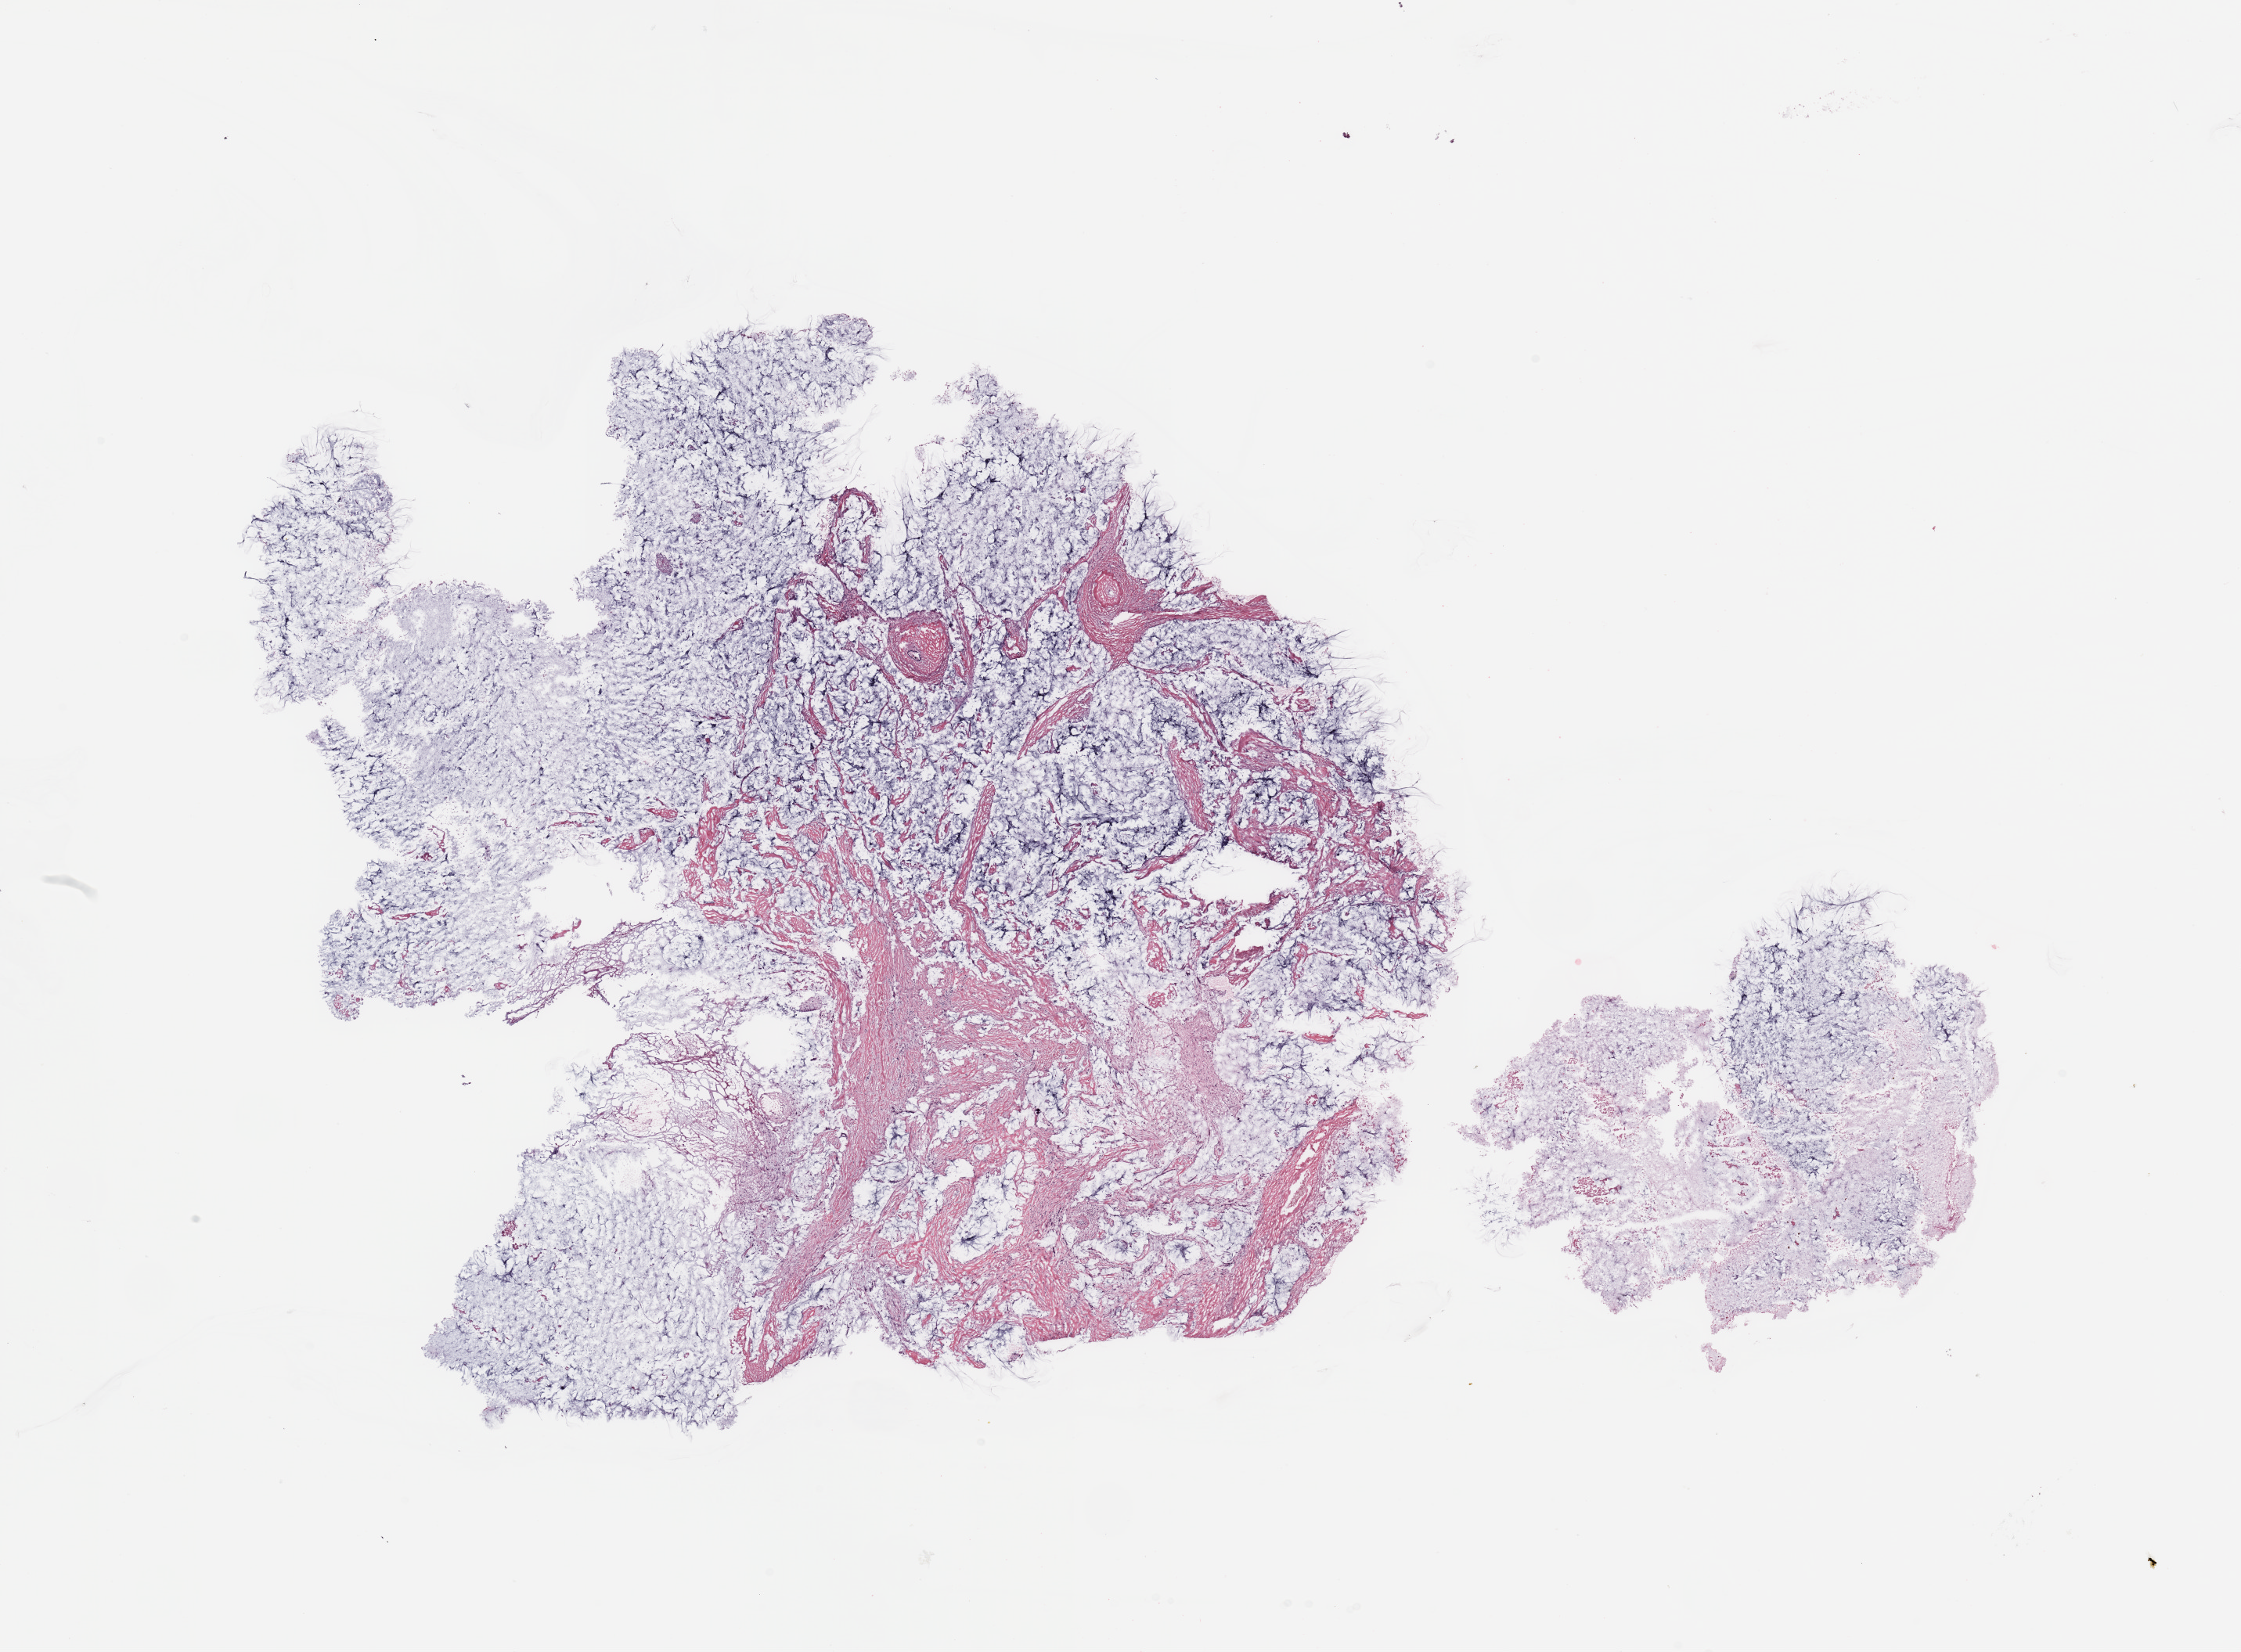
H&E-stained whole-slide image — a low-resolution overview of the entire scanned area, about 22.6 x 16.7 mm (from a 20x scan); breast, tissue type not recorded.
• patient diagnosis (cohort enrolment): breast cancer (breast)